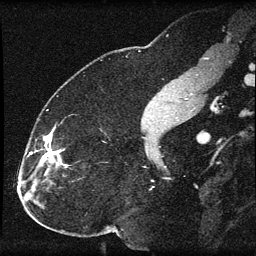
Breast MRI (dynamic contrast-enhanced), one sagittal slice; dynamic contrast-enhanced series, image 2 of 3 at this slice position (ordered by acquisition); 1.5 T; TE 4.2 ms, TR 8.2 ms; 2 mm slice thickness; 256 × 256 image matrix, field of view 180 × 180 mm. Patient: female, 32 years.
Outlined on this slice (semi-automatic segmentation, software-assisted and operator-edited):
- analysis volume of interest (the breast-tissue region the enhancement analysis was run in; not a lesion): bounding box <31,129,74,184> (left, top, right, bottom; pixels)
- tumour enhancement mask (voxels above the 70 % enhancement threshold inside the analysis volume of interest): <31,136,60,162>